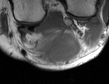
MRI of an extremity soft-tissue mass, one axial slice; slice 15 of 50 in the series (ordered by position); MR volume resampled by the dataset authors to the PET/CT grid (not the native acquisition matrix); 3.27 mm slice thickness; 109 × 84 image matrix. Male patient. From the clinical record (not read from this slice): histological type: synovial sarcoma; site of the primary tumour: left poplietal fossa.
Structures marked on this image (expert contour drawn on MRI and transferred to this co-registered scan by the dataset authors):
- gross tumour volume (mass): bounding box [x1, y1, x2, y2] px = [36, 32, 79, 63]